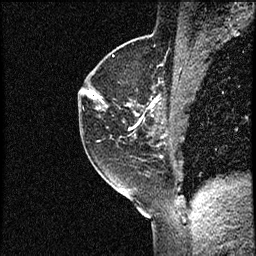
Breast MRI (dynamic contrast-enhanced), one sagittal slice. Slice 39 of 56 in the series (ordered by position). Dynamic contrast-enhanced study with each time point stored as its own series, time point 2 of 3 at this slice position (early post-contrast, ordered by acquisition time). 1.5 T. TE 4.2 ms, TR 17.3 ms. 2 mm slice thickness. 256 × 256 image matrix, field of view 200 × 200 mm. Female patient. Case-level facts recorded for this patient, not image findings: setting: breast cancer imaged before/during neoadjuvant chemotherapy; receptor status: HER2-positive.
Outlined on this slice (semi-automatic segmentation, software-assisted and operator-edited):
- analysis volume of interest (the breast-tissue region the enhancement analysis was run in; not a lesion): bounding box [x1, y1, x2, y2] px = [78, 50, 156, 155]
- tumour enhancement mask (voxels above the 100 % enhancement threshold inside the analysis volume of interest): [87, 91, 104, 103]